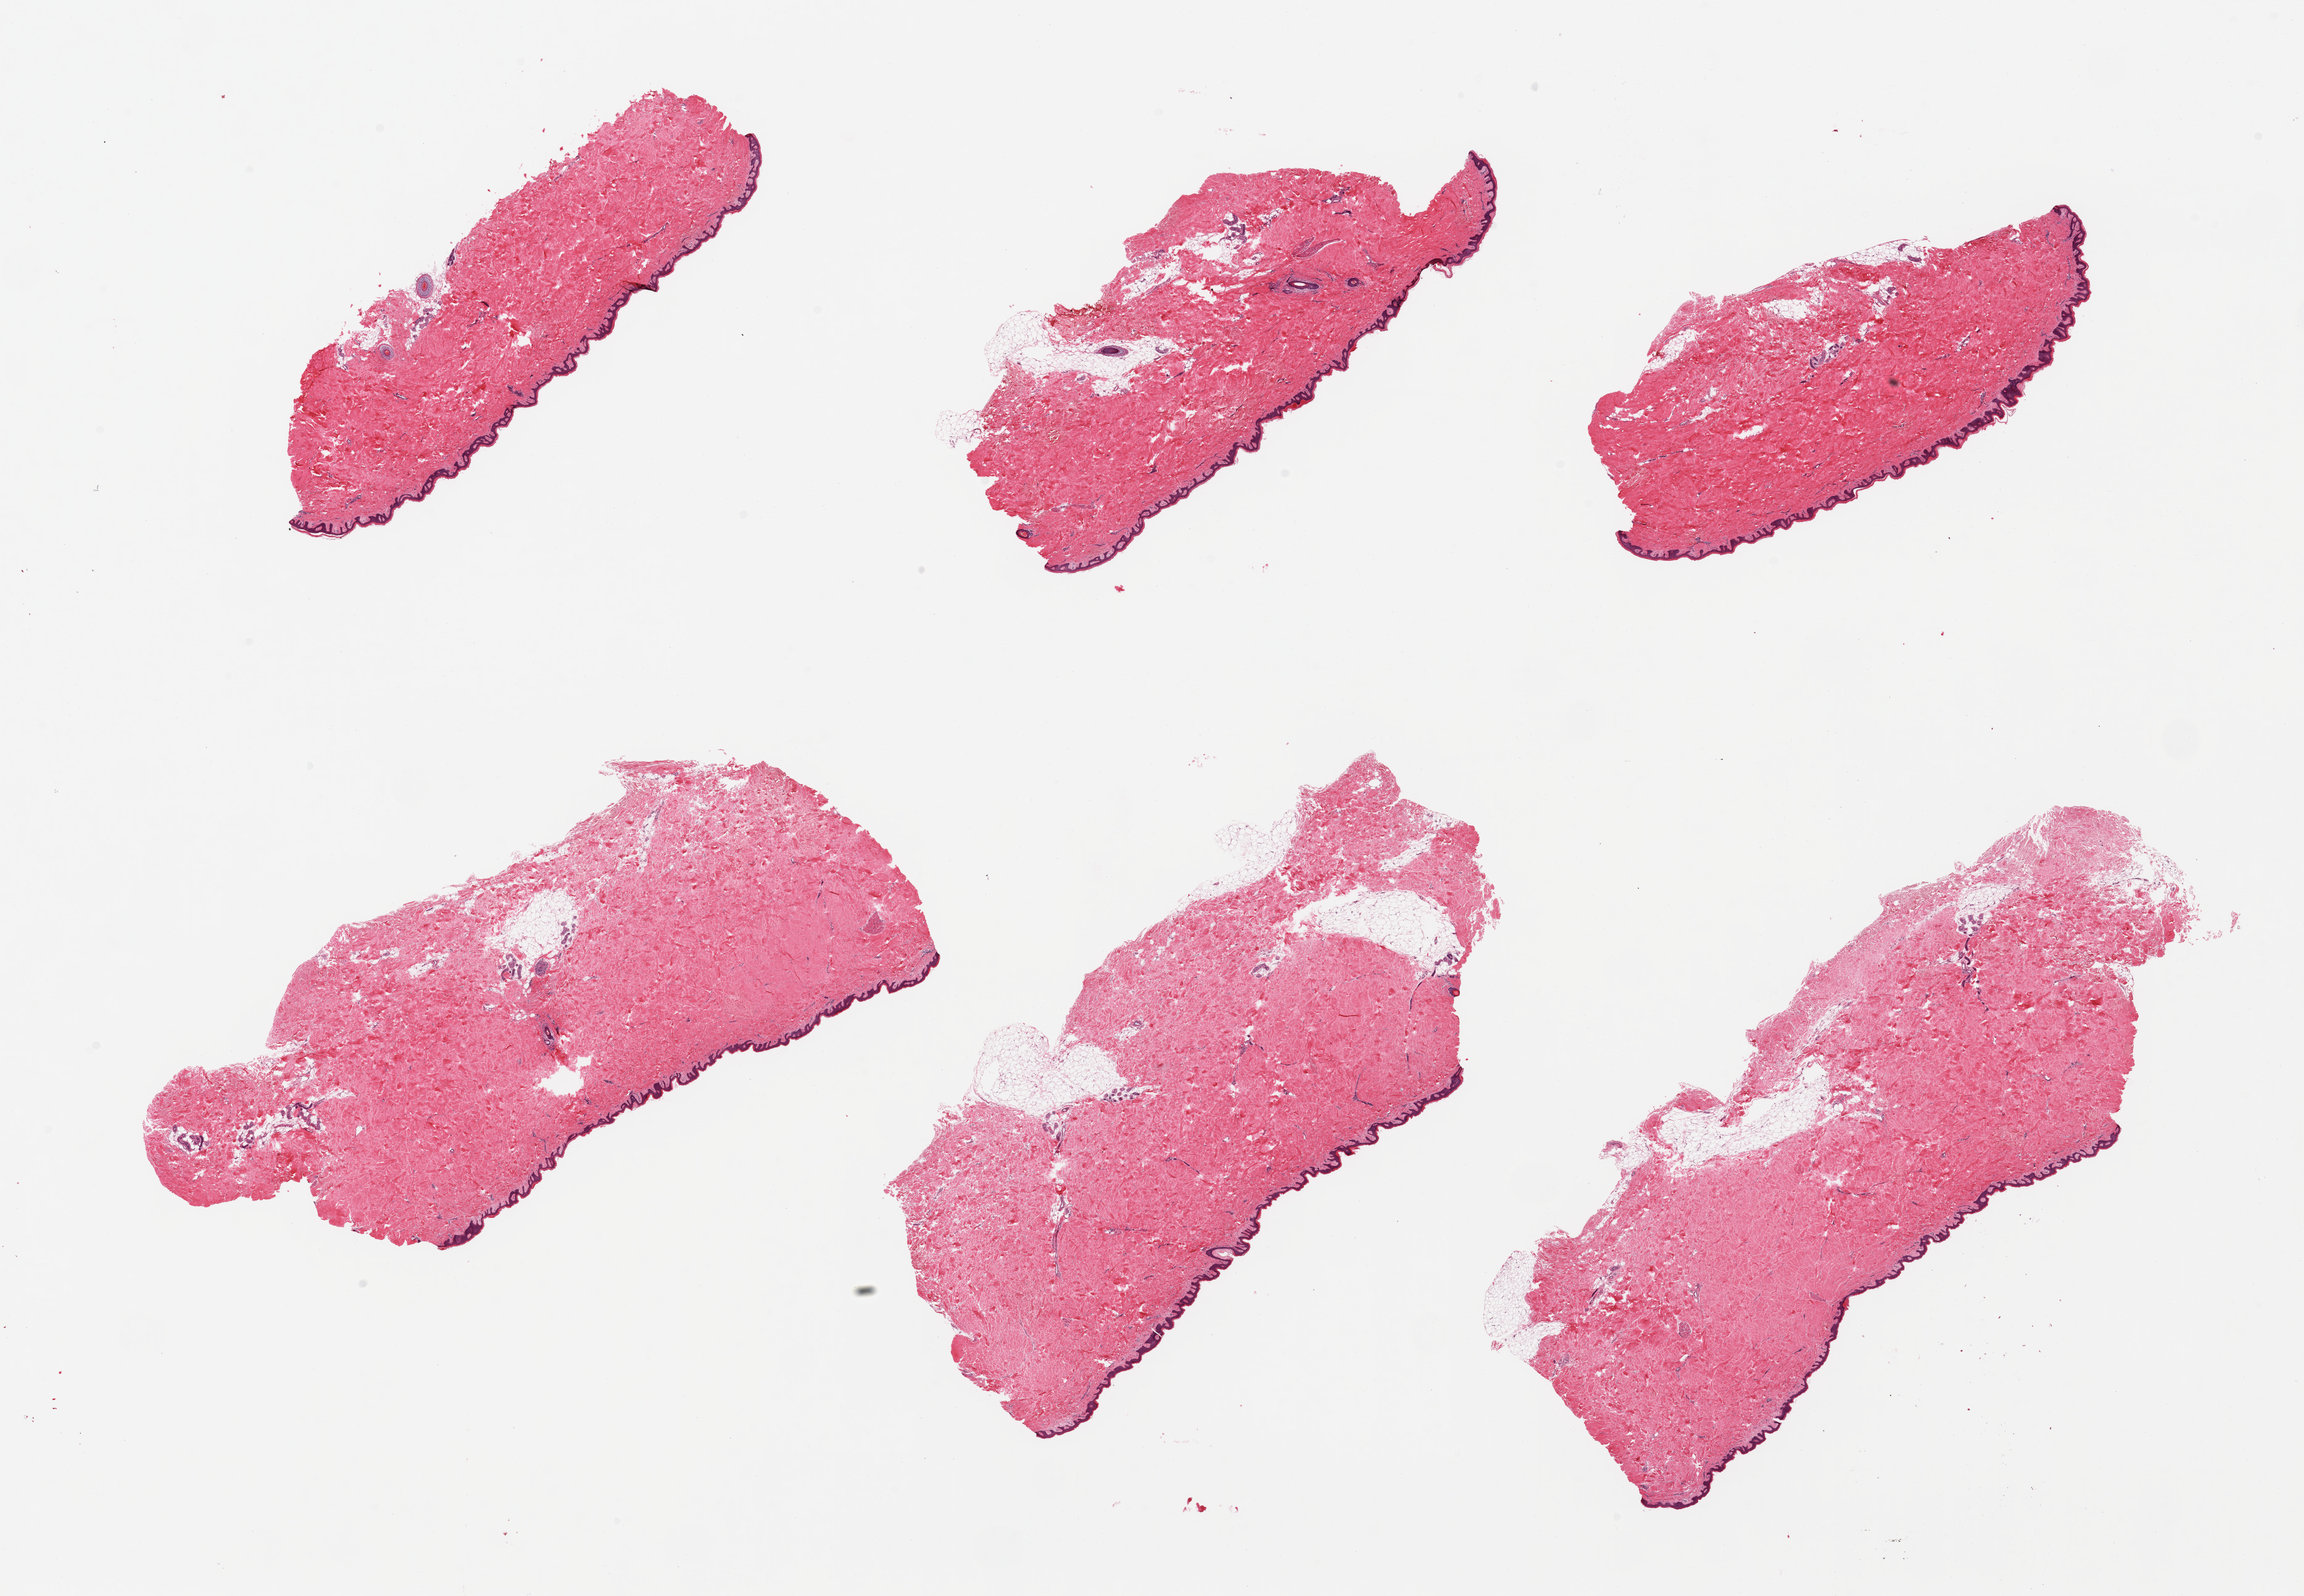
Haematoxylin and eosin whole-slide image — a low-resolution overview of the entire scanned area, about 29.5 x 20.5 mm, PAXgene-fixed, paraffin-embedded tissue, target tissue: skin of suprapubic region, tissue donor sample. Donor sex: female.
Reviewer comment on this tissue sample: 6 pieces; 10% intradermal fat; well dissected.